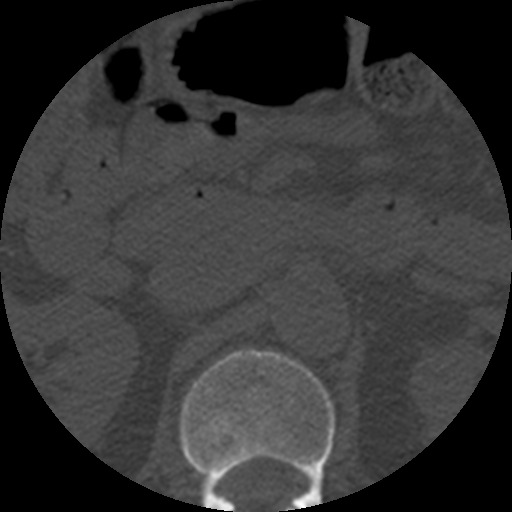
CT including the spine, one axial slice. Position 193 of 508 along the scan axis. Bone window (W 1800 / L 400 HU). 512 × 512 image matrix, field of view 160 × 160 mm. Patient age 57 years. From the clinical record (not read from this slice): primary cancer: prostate.
Structures marked on this image (semi-automatic segmentation, software-assisted and operator-edited):
- L1 vertebra: bounding box <179,349,336,512> (left, top, right, bottom; pixels)